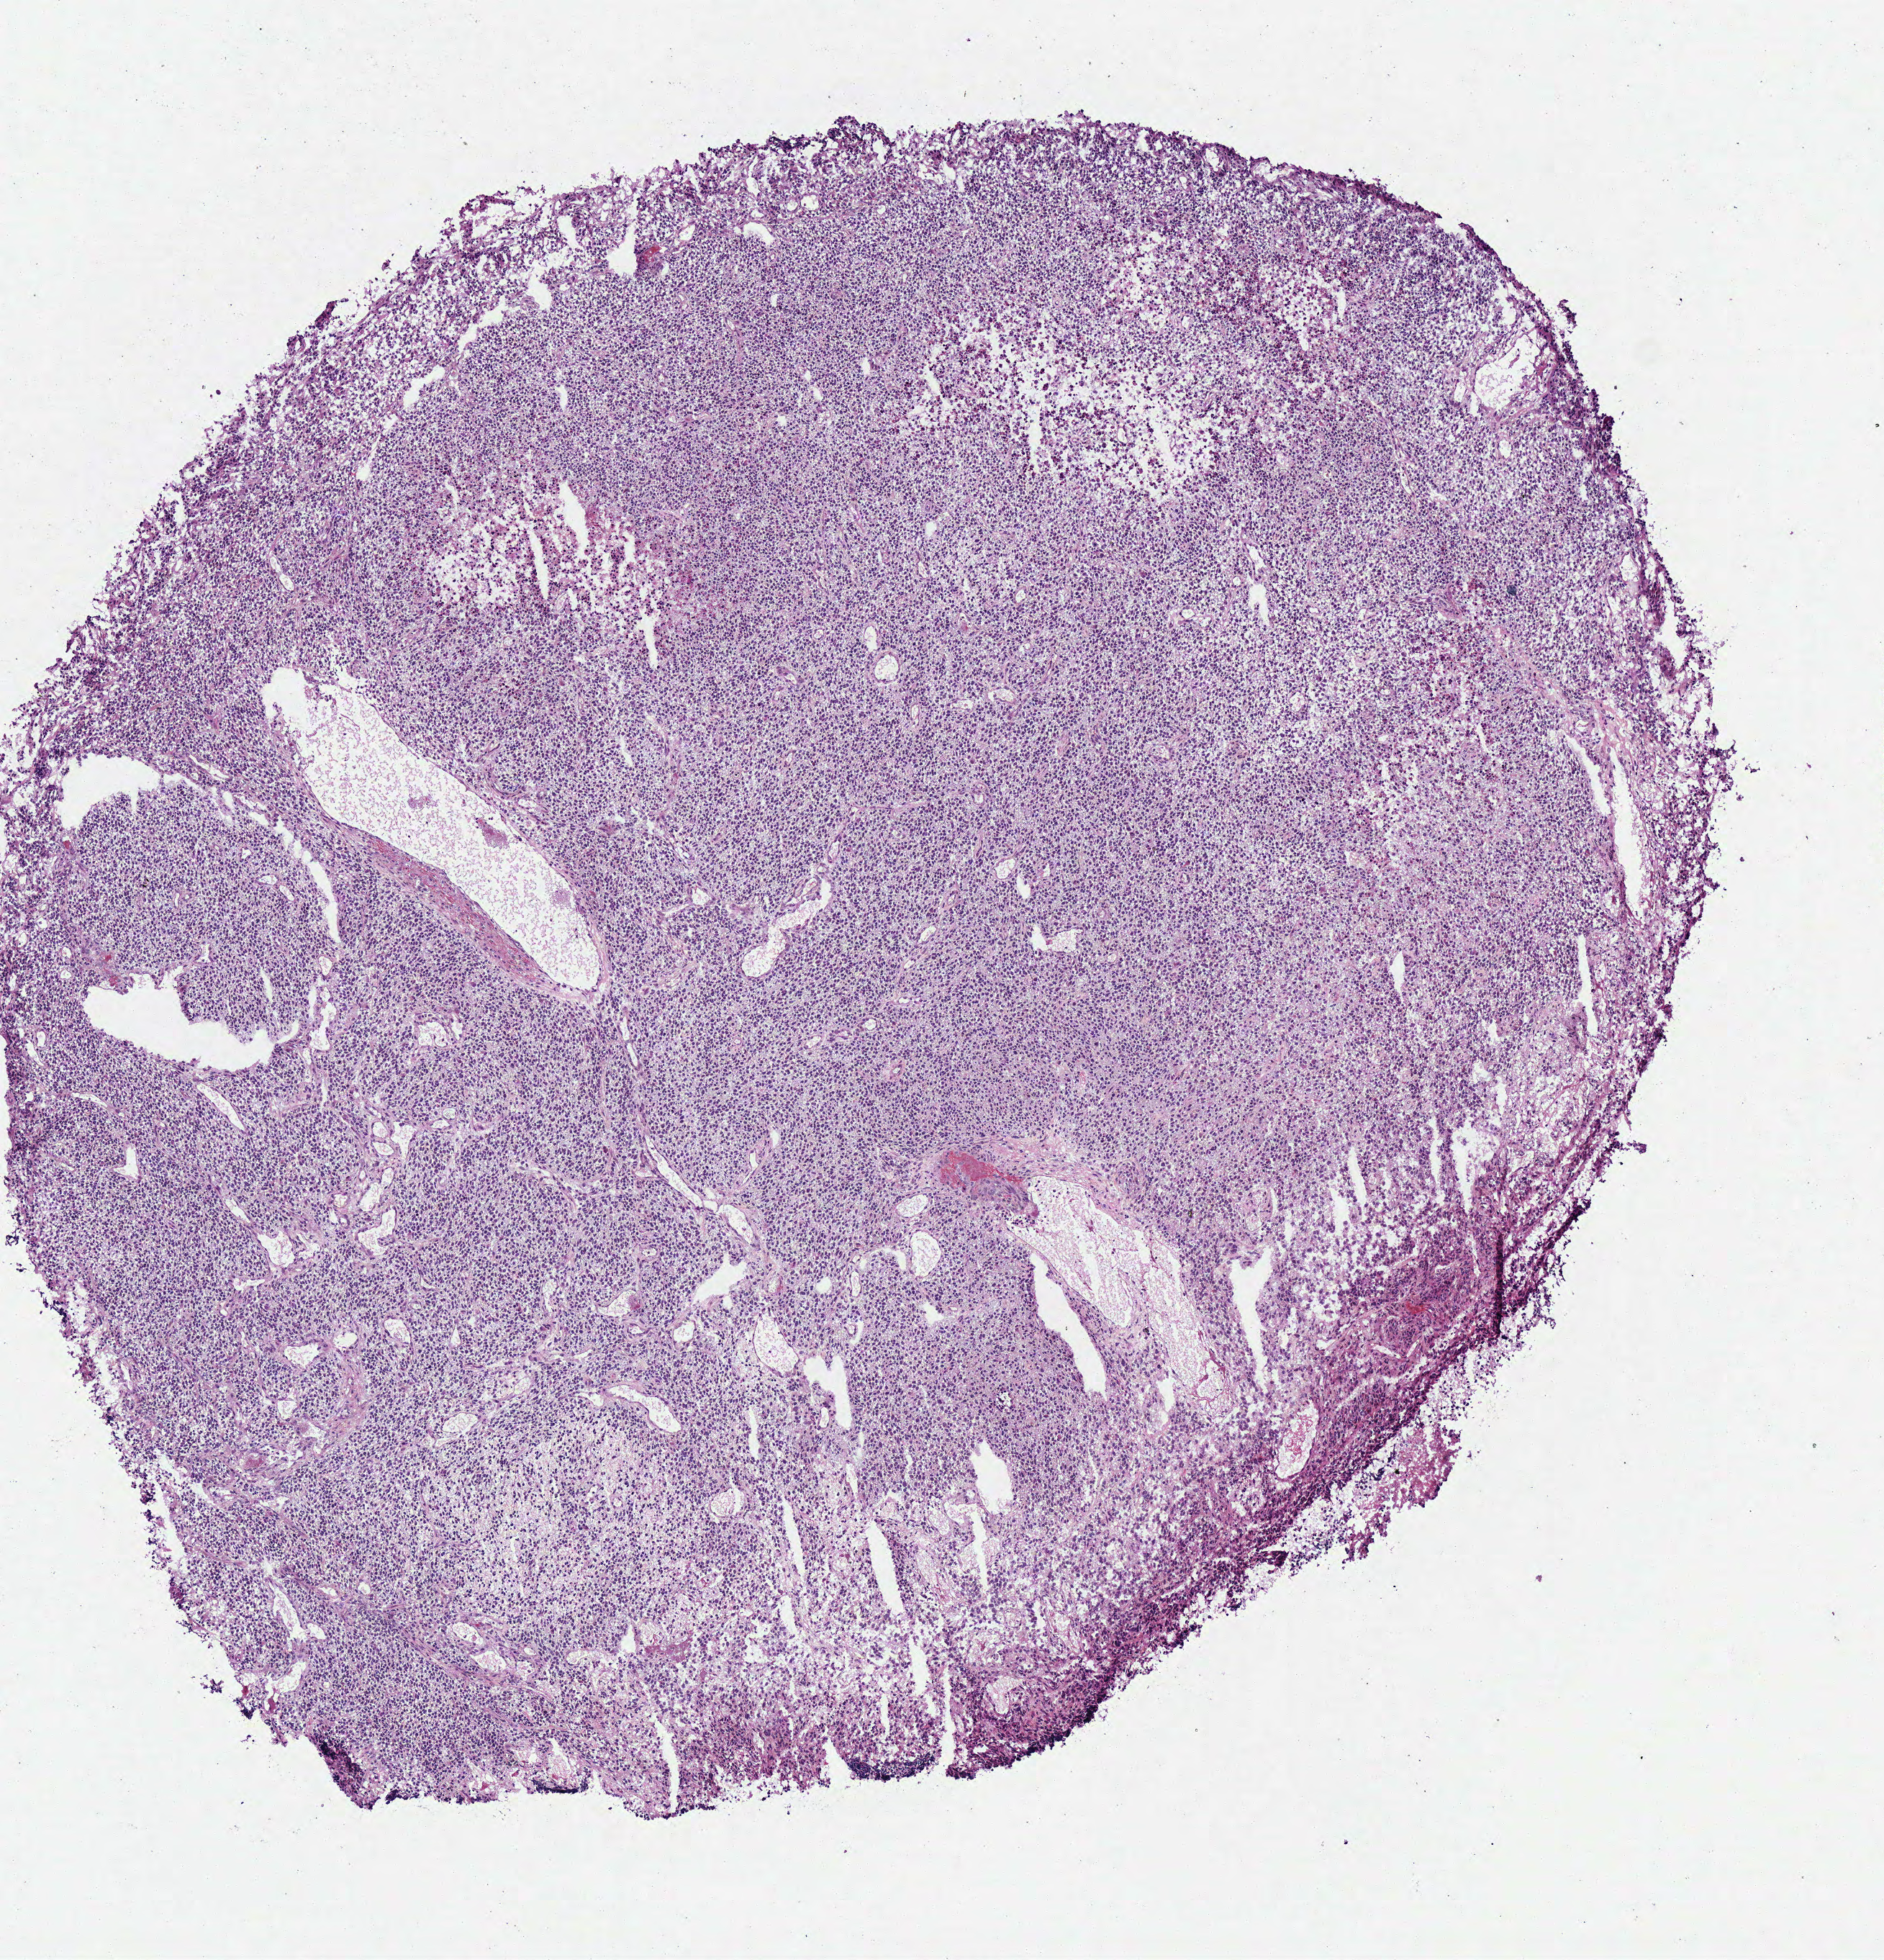
Digitized H&E tissue section (whole slide), a low-resolution overview of the entire scanned area, about 5.2 x 5.4 mm (slide scanned at 40x), frozen section from the top of the tissue portion, brain, primary tumour sample. Male, age 52 years at initial diagnosis. Composition of this section per pathologist review: tumour cells 90%, tumour nuclei 85%, normal cells 0%, stromal cells 0%, necrosis 10%.
- histologic diagnosis: Glioblastoma